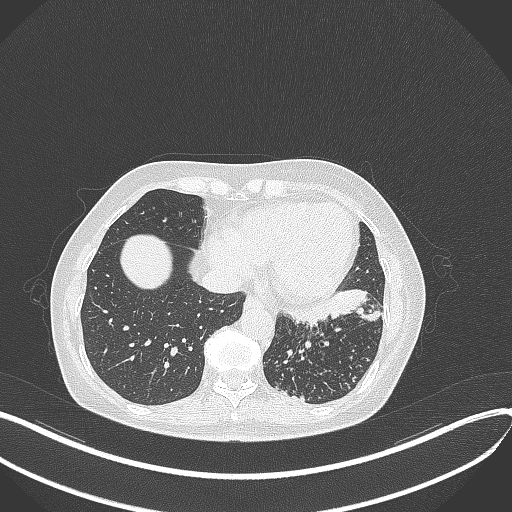
Chest CT, one axial slice. Reconstruction kernel B70f. Lung window (W 1500 / L -600 HU). 1 mm slice thickness. 512 × 512 image matrix. Female patient, age 63 years. From the clinical record (not read from this slice): clinical TNM (as recorded): T1b N0 M0.
Annotated regions visible in this slice (rectangle marked by the reading radiologist):
- lung tumour (recorded histology: adenocarcinoma): bounding box <284,290,382,331> (left, top, right, bottom; pixels)